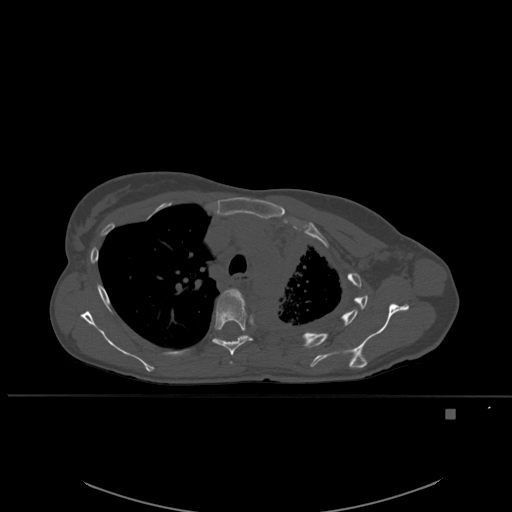
CT including the spine, one axial slice; position 399 of 537 along the scan axis; bone window (W 1800 / L 400 HU); 512 × 512 image matrix, field of view 440 × 440 mm. Patient: female, 45 years. From the clinical record (not read from this slice): primary cancer: lung.
Outlined on this slice (semi-automatically segmented with operator editing):
- T4 vertebra: bounding box (x1, y1, x2, y2) in pixels: (230, 288, 239, 364)
- T5 vertebra: (212, 289, 253, 356)
- T6 vertebra: (216, 338, 220, 339)